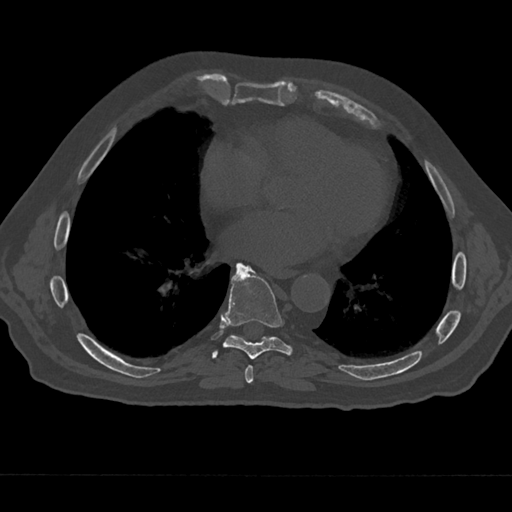
CT including the spine, one axial slice. Slice 312 of 797 in the series (ordered by position). 120 kVp. Bone window (W 1800 / L 400 HU). 512 × 512 image matrix. Male patient, age 75 years. From the clinical record (not read from this slice): primary cancer: renal; vertebrae with lytic lesions (as recorded): T4.
Outlined on this slice (semi-automatically segmented with operator editing):
- T7 vertebra: bounding box (x1, y1, x2, y2) in pixels: (240, 365, 254, 384)
- T8 vertebra: (212, 264, 293, 359)